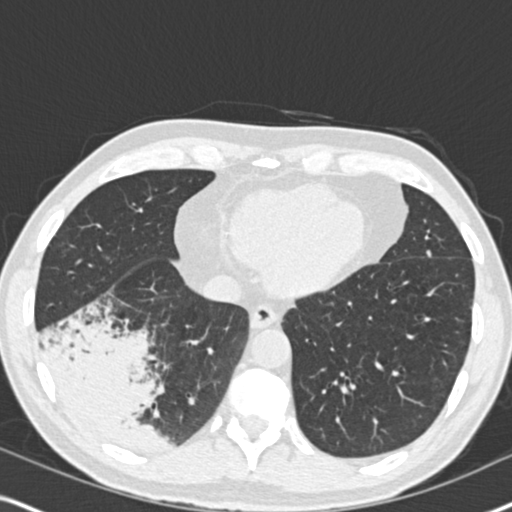
Low-dose screening chest CT, axial slice, second annual screen, lung window (W 1500 / L -600 HU), 2 mm slice thickness, 120 kVp, slice 120 of 182 in the series, 512 × 512 image matrix. Male participant, aged 61 years at enrolment. Current smoker at enrolment.
• Expert-annotated lung lesion, bounding box <34,302,185,459> (left, top, right, bottom; pixels).
• The exam's reader record, not a measurement of the box and not confirmed to be the same lesion: non-calcified nodule or mass ≥4 mm, right lower lobe, 90 × 80 mm, soft tissue attenuation, pre-existing on the prior screen: yes; interval growth: yes.
• Lung cancer was diagnosed 20 days after this screen: bronchiolo-alveolar adenocarcinoma, NOS, right lower lobe, moderately differentiated (G2), stage IIIB (AJCC 6th edition), 90 mm at pathology.